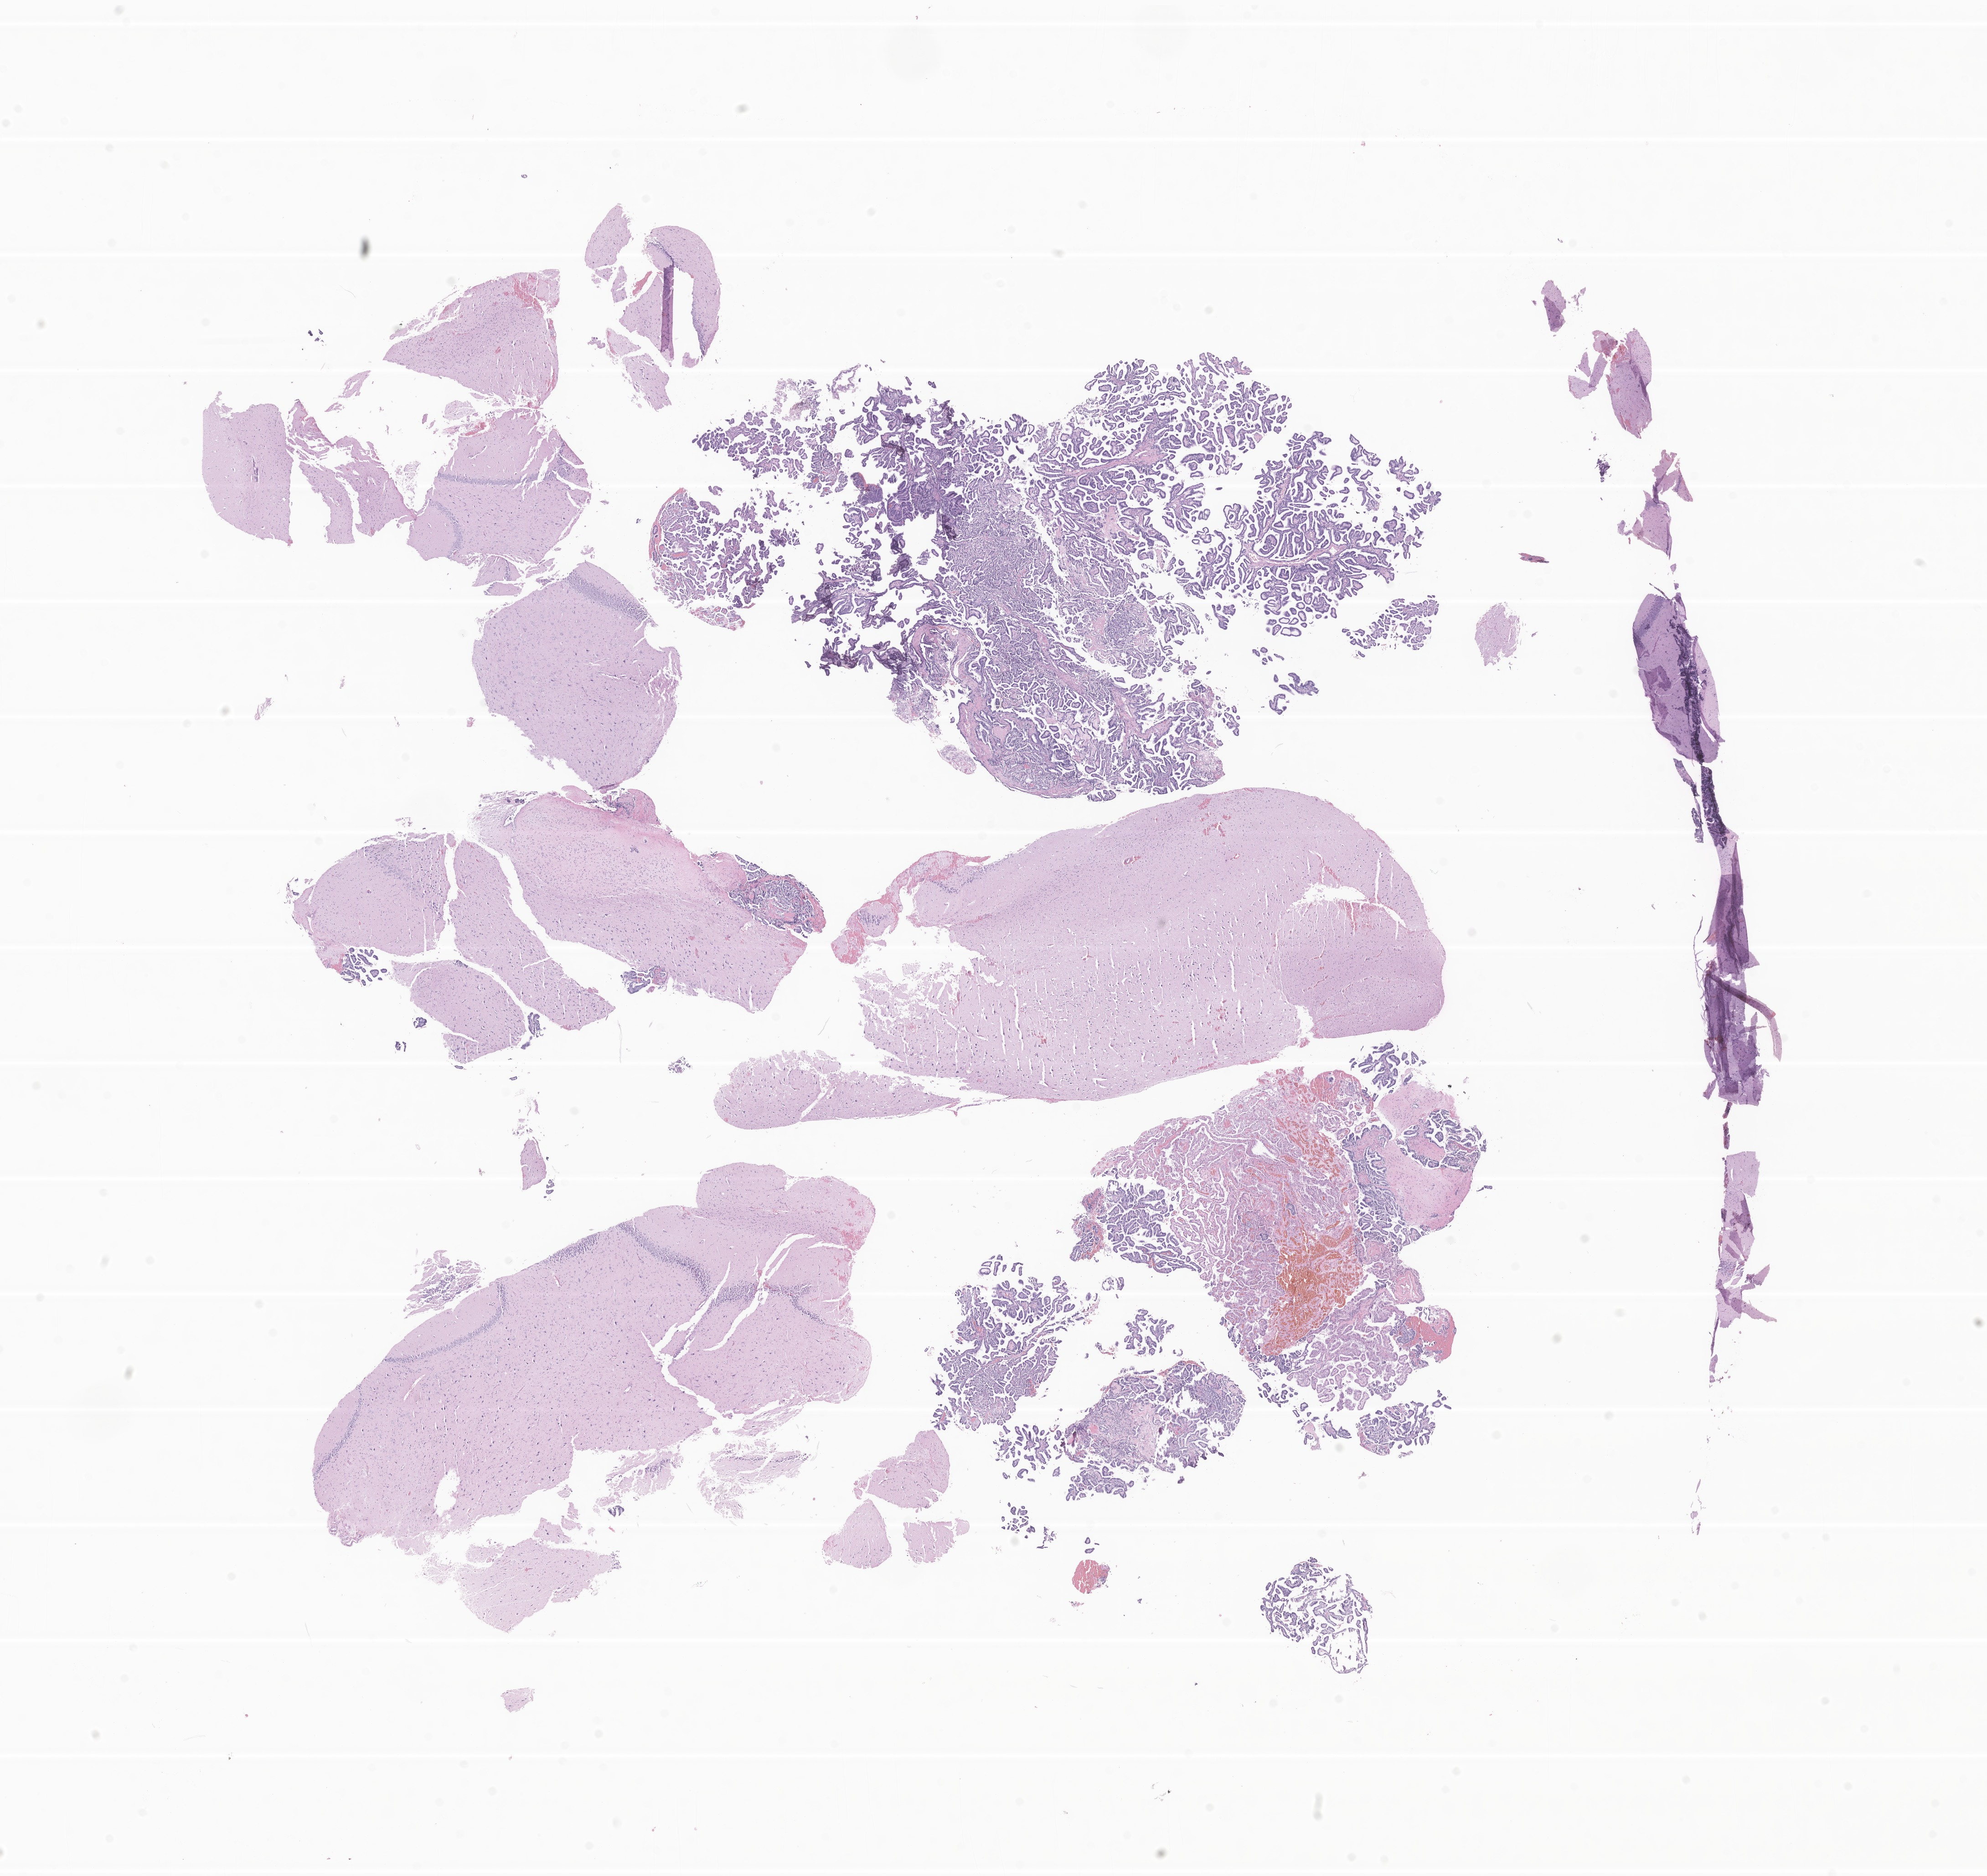
Whole-slide image, H&E stain of tumor tissue from the temporal lobe, shown as a low-resolution overview of the whole scanned area (about 18.4 x 17.4 mm); formalin-fixed, paraffin-embedded (FFPE) tissue. Patient: female, age 80 months (6 years 8 months).
Diagnosis: Choroid plexus papilloma, NOS.